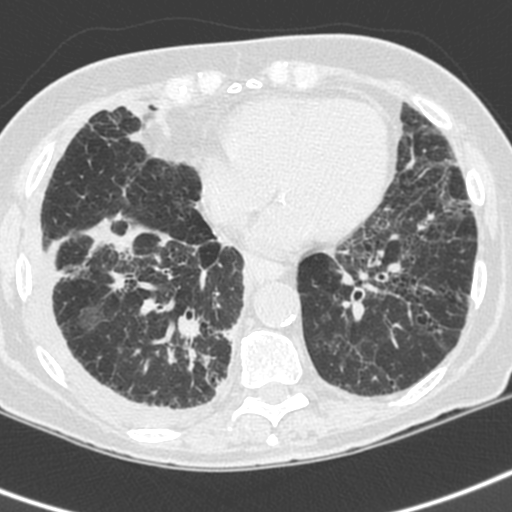
Axial slice from a low-dose chest CT screening exam; baseline screening round; lung window (W 1500 / L -600 HU); 1.3 mm slice thickness; 120 kVp; slice 129 of 192 in the series; 512 × 512 image matrix. Female participant, aged 73 years at enrolment. Current smoker at enrolment.
Lesion marked by an expert reader, bounding box (x1, y1, x2, y2) in pixels: (153, 313, 235, 406). Reader record for this screening exam (exam-level; its link to the box is not recorded): non-calcified nodule or mass ≥4 mm, right lower lobe, 35 × 30 mm, spiculated (stellate) margins, soft tissue attenuation. Official screen result: positive, change unspecified: nodule(s) >= 4 mm or enlarging nodule(s), mass(es), or other non-specific abnormalities suspicious for lung cancer. Participant outcome: lung cancer diagnosed 22 days after this screen — adenocarcinoma, NOS, right lower lobe, stage IV (AJCC 6th edition), 35 mm at pathology.